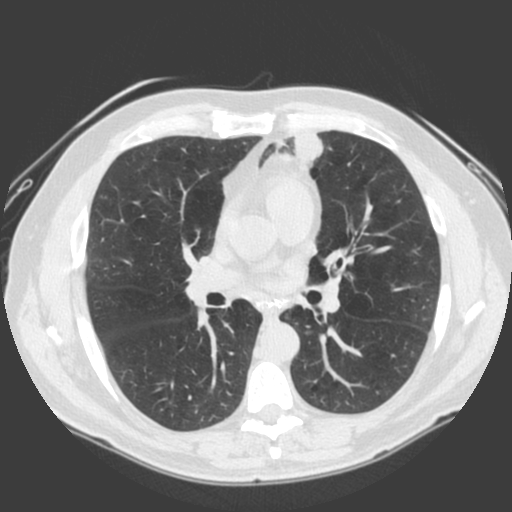
Low-dose screening chest CT, one axial slice. Slice 101 of 185 in the series (ordered by position). Lung window (W 1500 / L -600 HU). 2 mm slice thickness. 512 × 512 image matrix, field of view 360 × 360 mm.
Outlined on this slice (outlined manually by an expert reader):
- lesion 1 (tumor, lower lobe of left lung): bounding box [x1, y1, x2, y2] px = [291, 134, 324, 165]